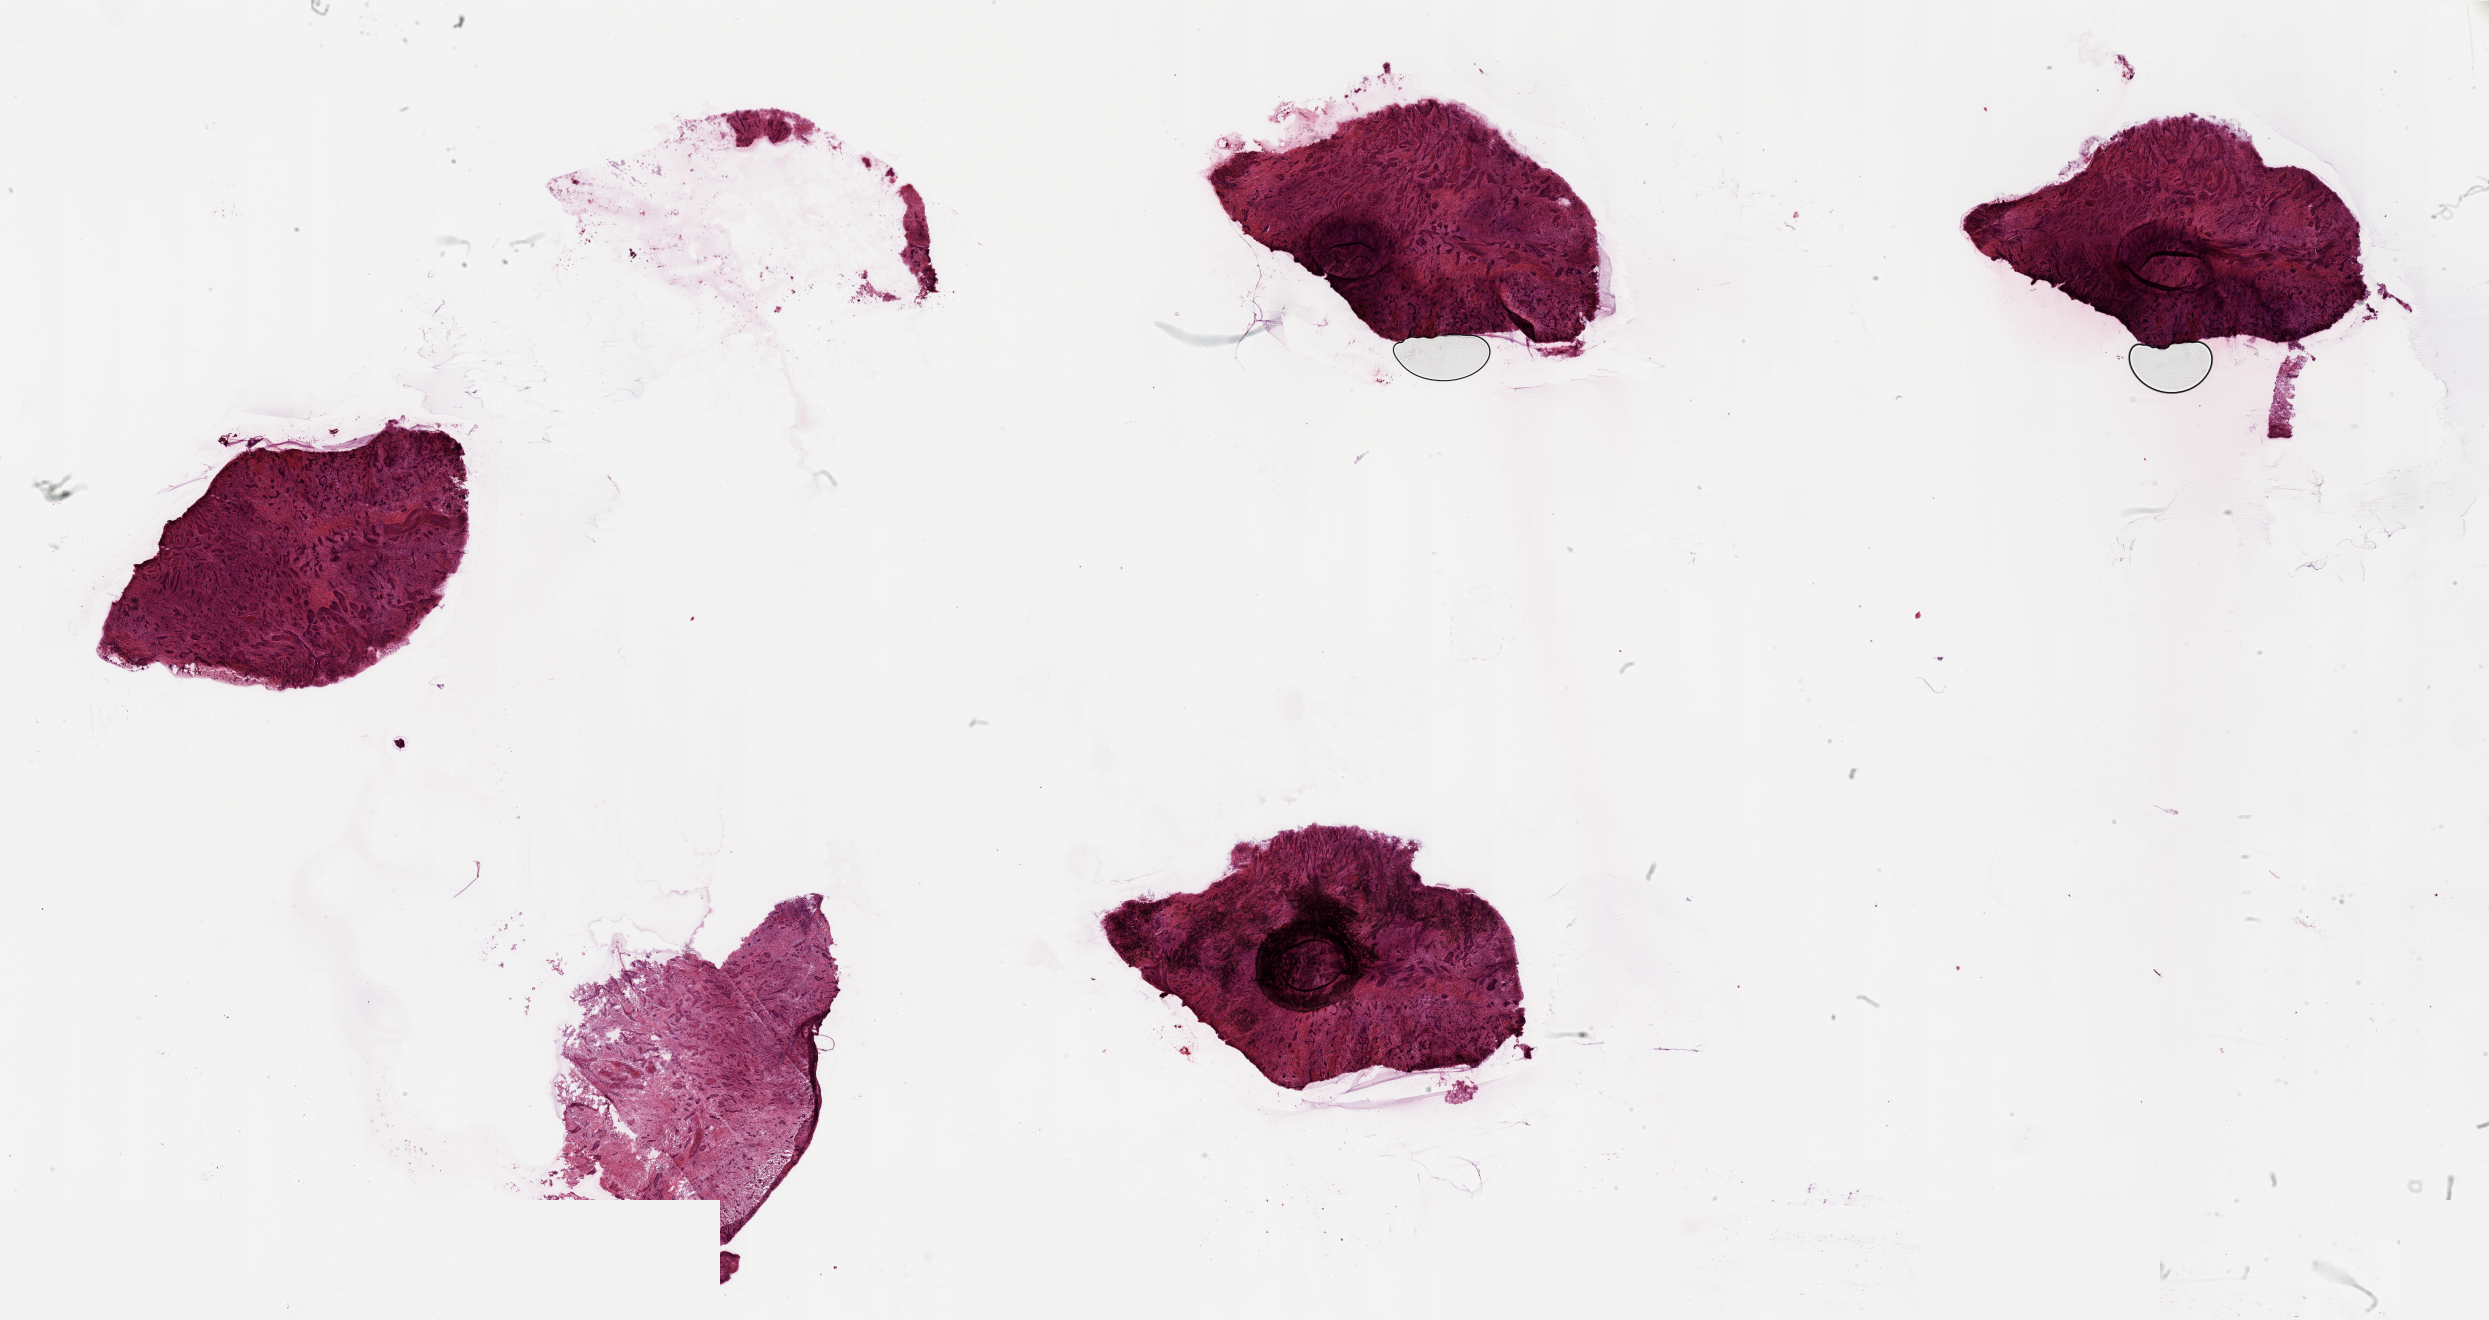
Hematoxylin and eosin (H&E) stained whole-slide image, low-resolution overview of the scanned area, about 39.4 x 20.9 mm, head and neck, tissue type not recorded. Male, 70 y/o.
Patient diagnosis: Squamous cell carcinoma, NOS.